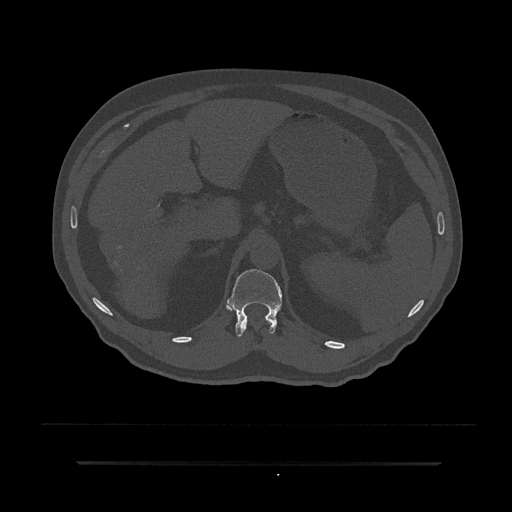
CT including the spine, one axial slice; position 227 of 797 along the scan axis; 120 kVp; bone window (W 1800 / L 400 HU); 0.5 mm slice thickness; 512 × 512 image matrix, field of view 464 × 464 mm. Patient: male, 59 years. Case-level facts recorded for this patient, not image findings: primary cancer: bile ducts.
Structures marked on this image (semi-automatically segmented with operator editing):
- T11 vertebra: bounding box [x1, y1, x2, y2] px = [244, 323, 247, 329]
- T12 vertebra: [227, 269, 282, 337]